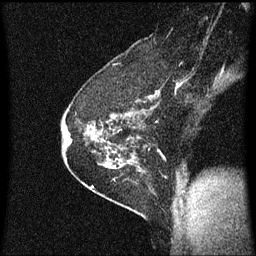
Breast MRI (dynamic contrast-enhanced), one sagittal slice; position 43 of 60 along the scan axis; dynamic contrast-enhanced series, image 2 of 3 at this slice position (ordered by acquisition); 1.5 T; TE 4.2 ms, TR 8.4 ms; 256 × 256 image matrix, field of view 200 × 200 mm. Patient: female, 60 years.
Outlined on this slice (semi-automatically segmented with operator editing):
- analysis volume of interest (the breast-tissue region the enhancement analysis was run in; not a lesion): bounding box <69,66,146,193> (left, top, right, bottom; pixels)
- tumour enhancement mask (voxels above the 70 % enhancement threshold inside the analysis volume of interest): <69,112,144,169>